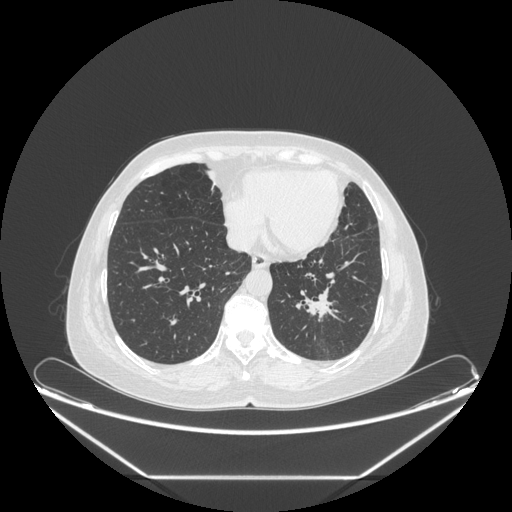
Chest CT, one axial slice; position 81 of 241 along the scan axis; reconstruction kernel STANDARD; 120 kVp; lung window (W 1500 / L -600 HU); 1.25 mm slice thickness; 512 × 512 image matrix. Patient: female, 63 years. Case-level facts recorded for this patient, not image findings: clinical TNM (as recorded): T1c N0 M0; histopathological grade: G2-3.
Structures marked on this image (bounding box drawn by a radiologist):
- lung tumour (recorded histology: adenocarcinoma): box from (x=297, y=283) to (x=337, y=324) px